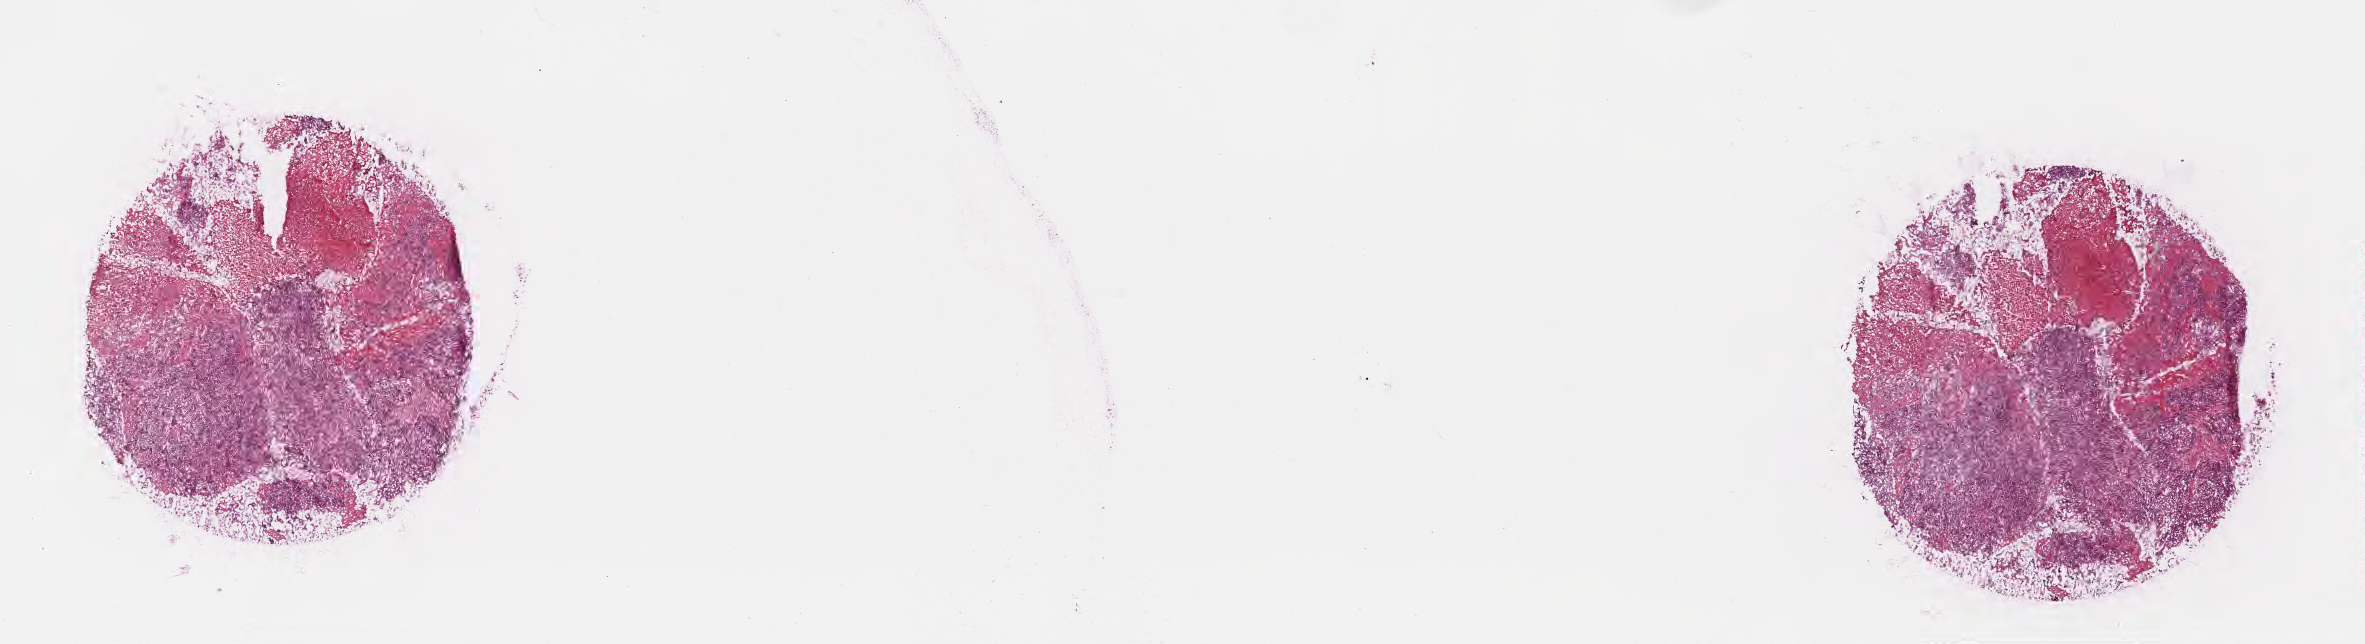
Hematoxylin and eosin (H&E) whole-slide image, low-resolution overview of the scanned area, about 19.1 x 5.2 mm; cryosection; specimen: primary tumor; anatomic site: splenic flexure of colon. Female, age 81 years at initial diagnosis. Pathologist review of this section (percent, as recorded): tumor cells 55%, tumor nuclei 55%.
Histologic diagnosis: Medullary carcinoma, NOS.